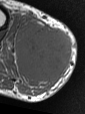
MRI of an extremity soft-tissue mass, one axial slice. Position 27 of 47 along the scan axis. MR volume resampled by the dataset authors to the PET/CT grid (not the native acquisition matrix). 3.27 mm slice thickness. 85 × 114 image matrix, field of view 83 × 111 mm. Male patient. From the clinical record (not read from this slice): histological type: pleiomorphic liposarcoma; grade: high; site of the primary tumour: right calf.
Annotated regions visible in this slice (expert contour drawn on MRI and transferred to this co-registered scan by the dataset authors):
- gross tumour volume including surrounding oedema: bounding box <17,23,71,85> (left, top, right, bottom; pixels)
- gross tumour volume (mass): <17,25,71,81>